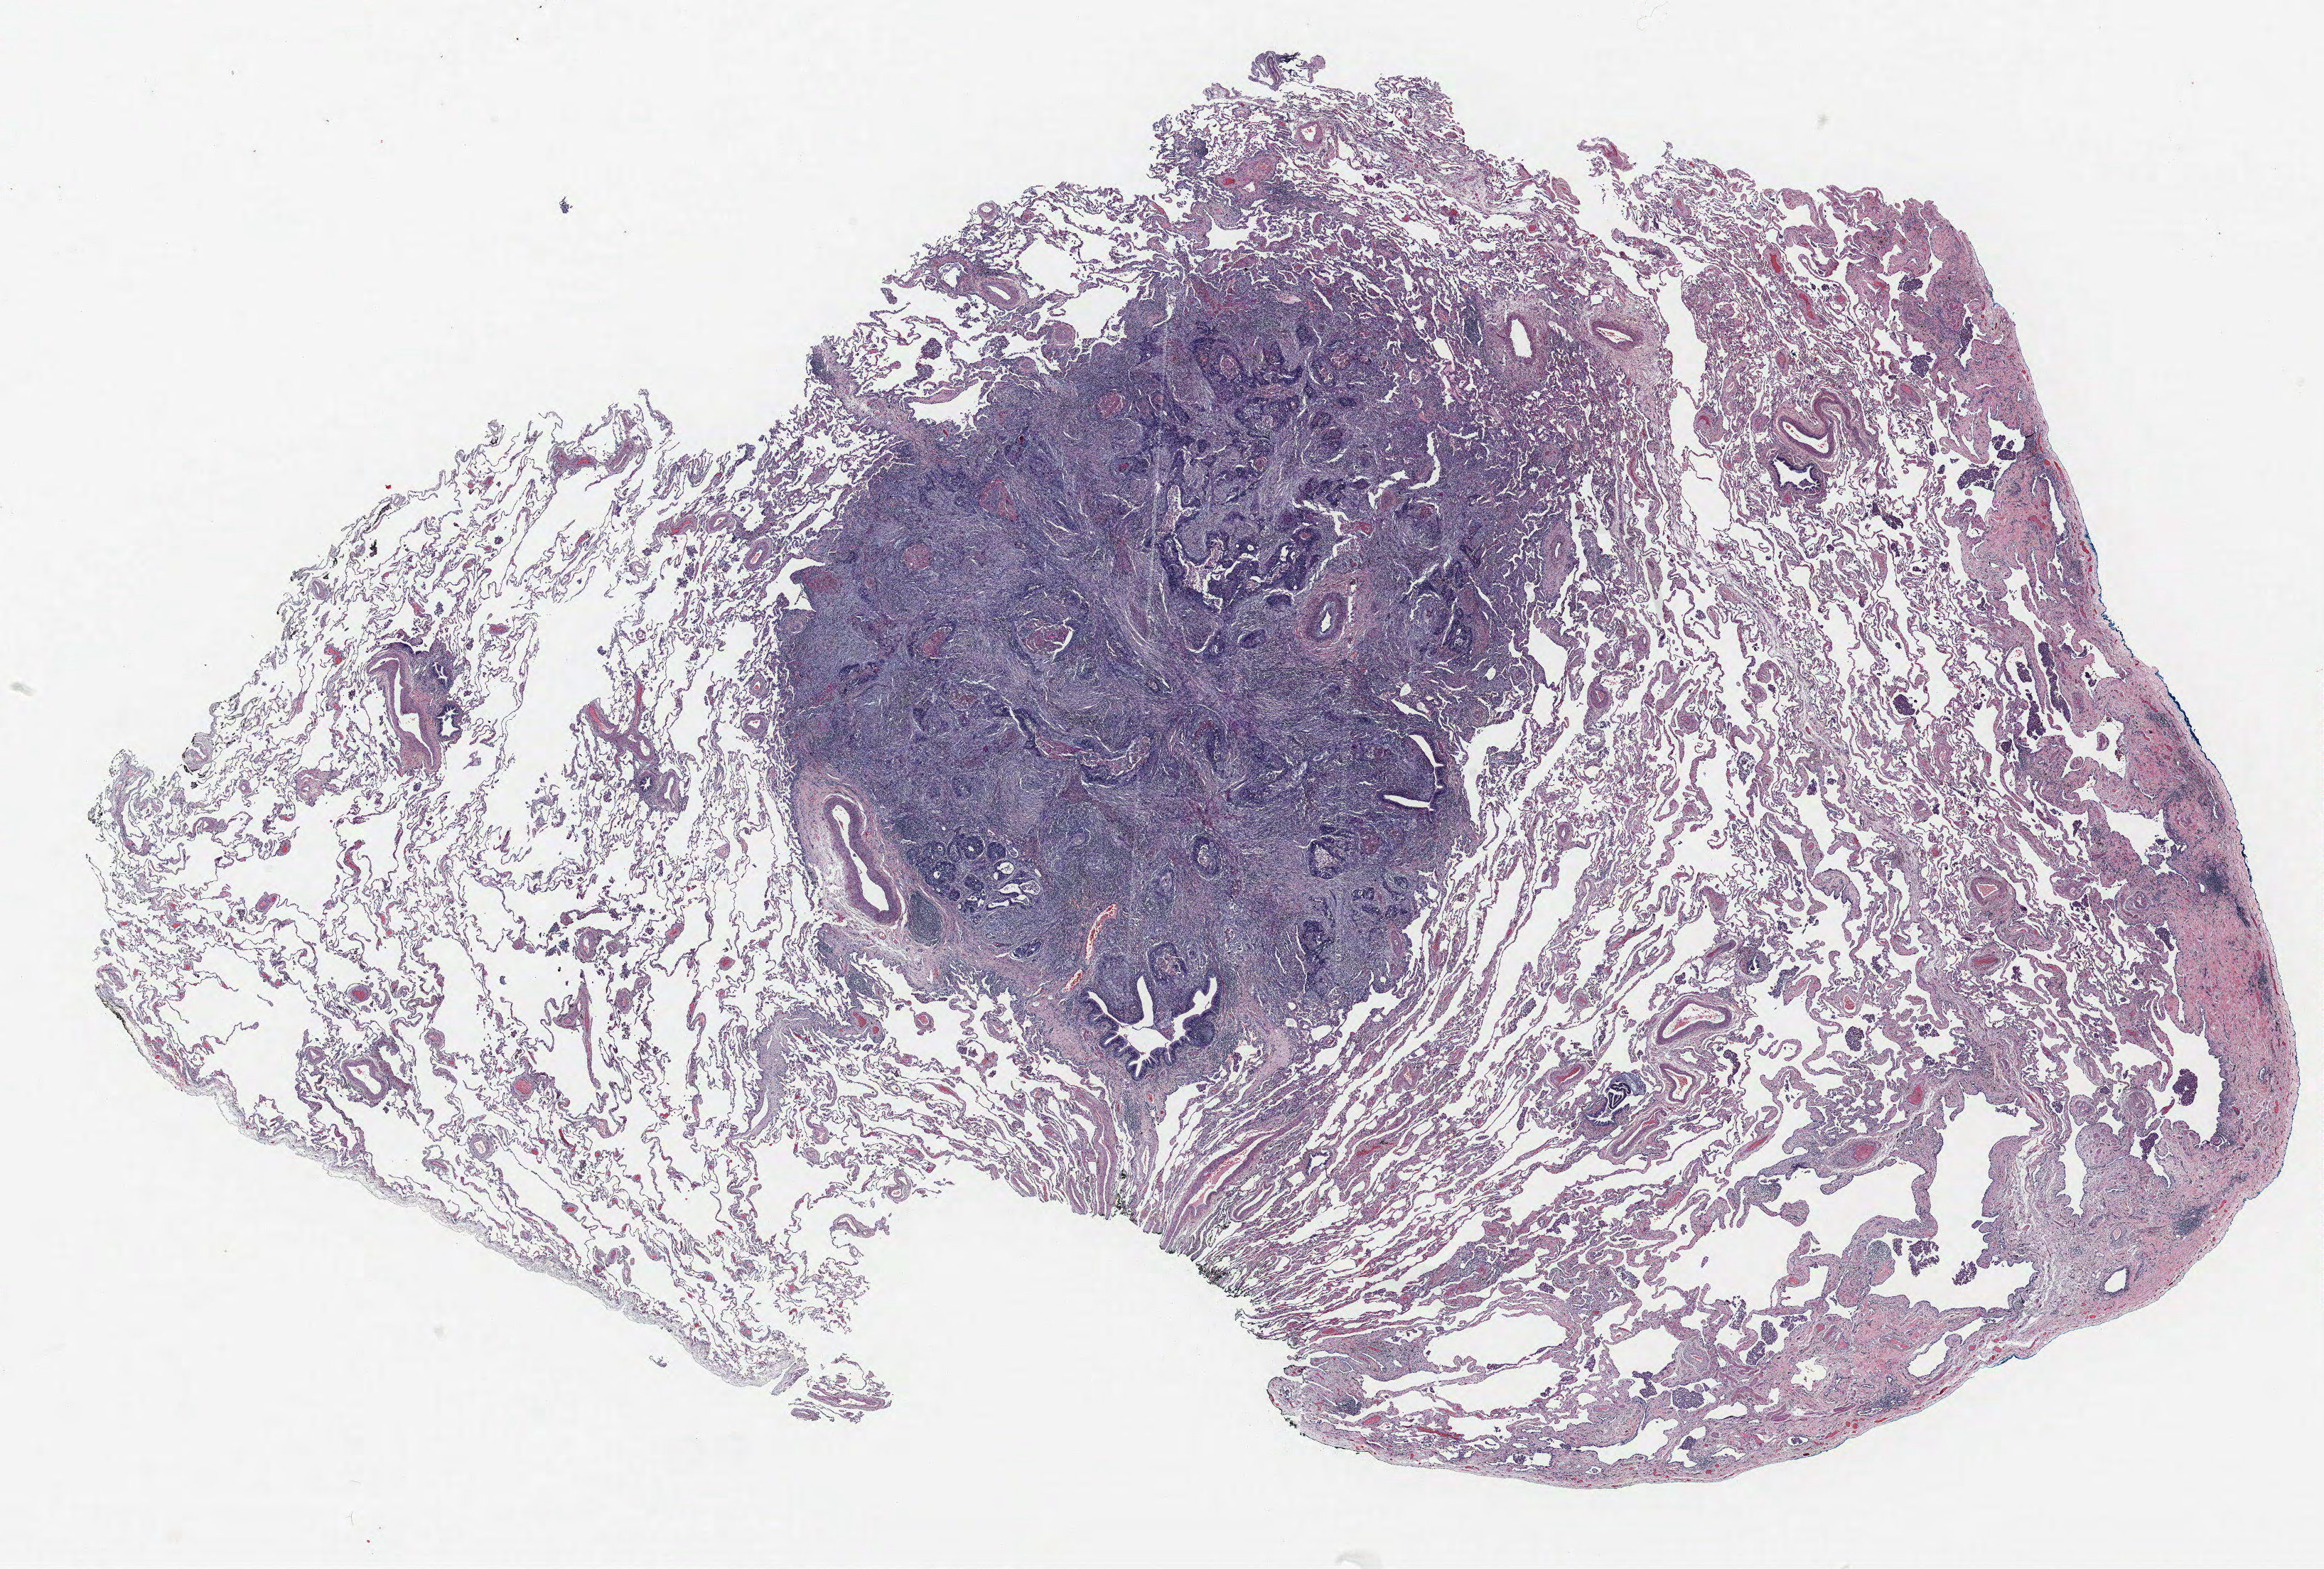
H&E-stained whole-slide image, whole scanned area (about 26.2 x 17.7 mm, from a 40x scan) shown as a low-resolution overview. Formalin-fixed paraffin-embedded (FFPE) section. Lung tissue. Male patient, aged 62 at enrolment. Grade: moderately differentiated (G2).
Stage (AJCC 6th edition): IA. Tumour size (pathology): 17 mm. Primary tumour location (clinical record): left upper lobe. Participant's lung-cancer diagnosis: Squamous cell carcinoma, NOS. ICD-O-3 topography: upper lobe of lung (C34.1).